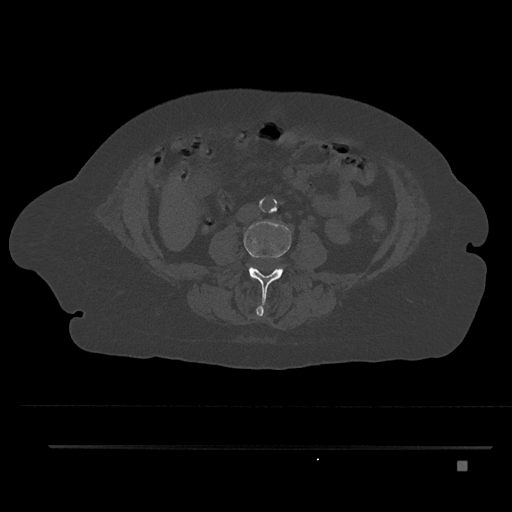
CT including the spine, one axial slice. Slice 122 of 797 in the series (ordered by position). Reconstruction kernel Br40s/3. 120 kVp. Bone window (W 1800 / L 400 HU). 512 × 512 image matrix, field of view 437 × 437 mm. Patient: female, 76 years. From the clinical record (not read from this slice): primary cancer: lung; vertebrae with lytic lesions (as recorded): T11, L3.
Outlined on this slice (semi-automatic segmentation, software-assisted and operator-edited):
- L2 vertebra: bounding box <256,306,264,318> (left, top, right, bottom; pixels)
- L3 vertebra: <244,220,291,306>